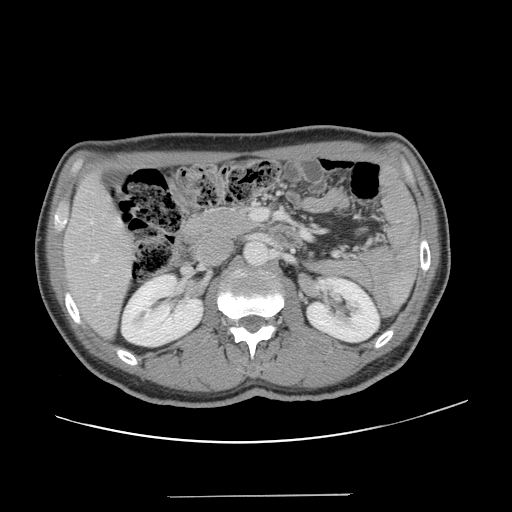
Contrast-enhanced abdominal CT, one axial slice. Slice 63 of 131 in the series (ordered by position). 120 kVp. Intravenous contrast given. Soft-tissue window (W 400 / L 40 HU). 2.5 mm slice thickness. 512 × 512 image matrix, field of view 403 × 403 mm. Male patient, age 60 years. Case-level facts recorded for this patient, not image findings: diagnosis: colorectal cancer liver metastases, imaged before liver resection; multiple liver metastases: no; largest metastasis: 2.5 cm; disease in both lobes: no.
Structures marked on this image (expert manual segmentation):
- hepatic veins: bounding box <91,222,100,299> (left, top, right, bottom; pixels)
- liver: <65,177,131,336>
- planned liver remnant (the part of the liver to remain after resection): <65,177,131,336>